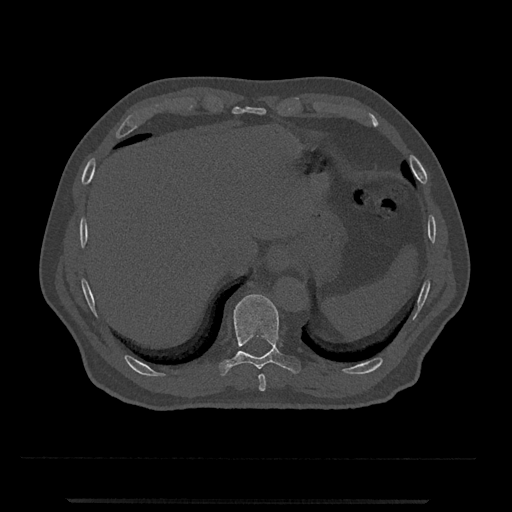
CT including the spine, one axial slice. Slice 522 of 797 in the series (ordered by position). Reconstruction kernel Br40s/3. 120 kVp. Bone window (W 1800 / L 400 HU). 0.5 mm slice thickness. 512 × 512 image matrix. Patient: male, 63 years. Case-level facts recorded for this patient, not image findings: primary cancer: prostate.
Outlined on this slice (semi-automatic segmentation, software-assisted and operator-edited):
- T10 vertebra: bounding box [x1, y1, x2, y2] px = [219, 294, 301, 376]
- T9 vertebra: [258, 374, 266, 392]